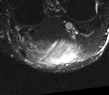
MRI of an extremity soft-tissue mass, one axial slice; position 13 of 52 along the scan axis; T2-weighted fat-saturated; MR volume resampled by the dataset authors to the PET/CT grid (not the native acquisition matrix); 3.27 mm slice thickness; 109 × 95 image matrix. Male patient. Case-level facts recorded for this patient, not image findings: histological type: synovial sarcoma; site of the primary tumour: left poplietal fossa.
Structures marked on this image (expert contour drawn on MRI and transferred to this co-registered scan by the dataset authors):
- gross tumour volume (mass): box from (x=40, y=40) to (x=77, y=64) px